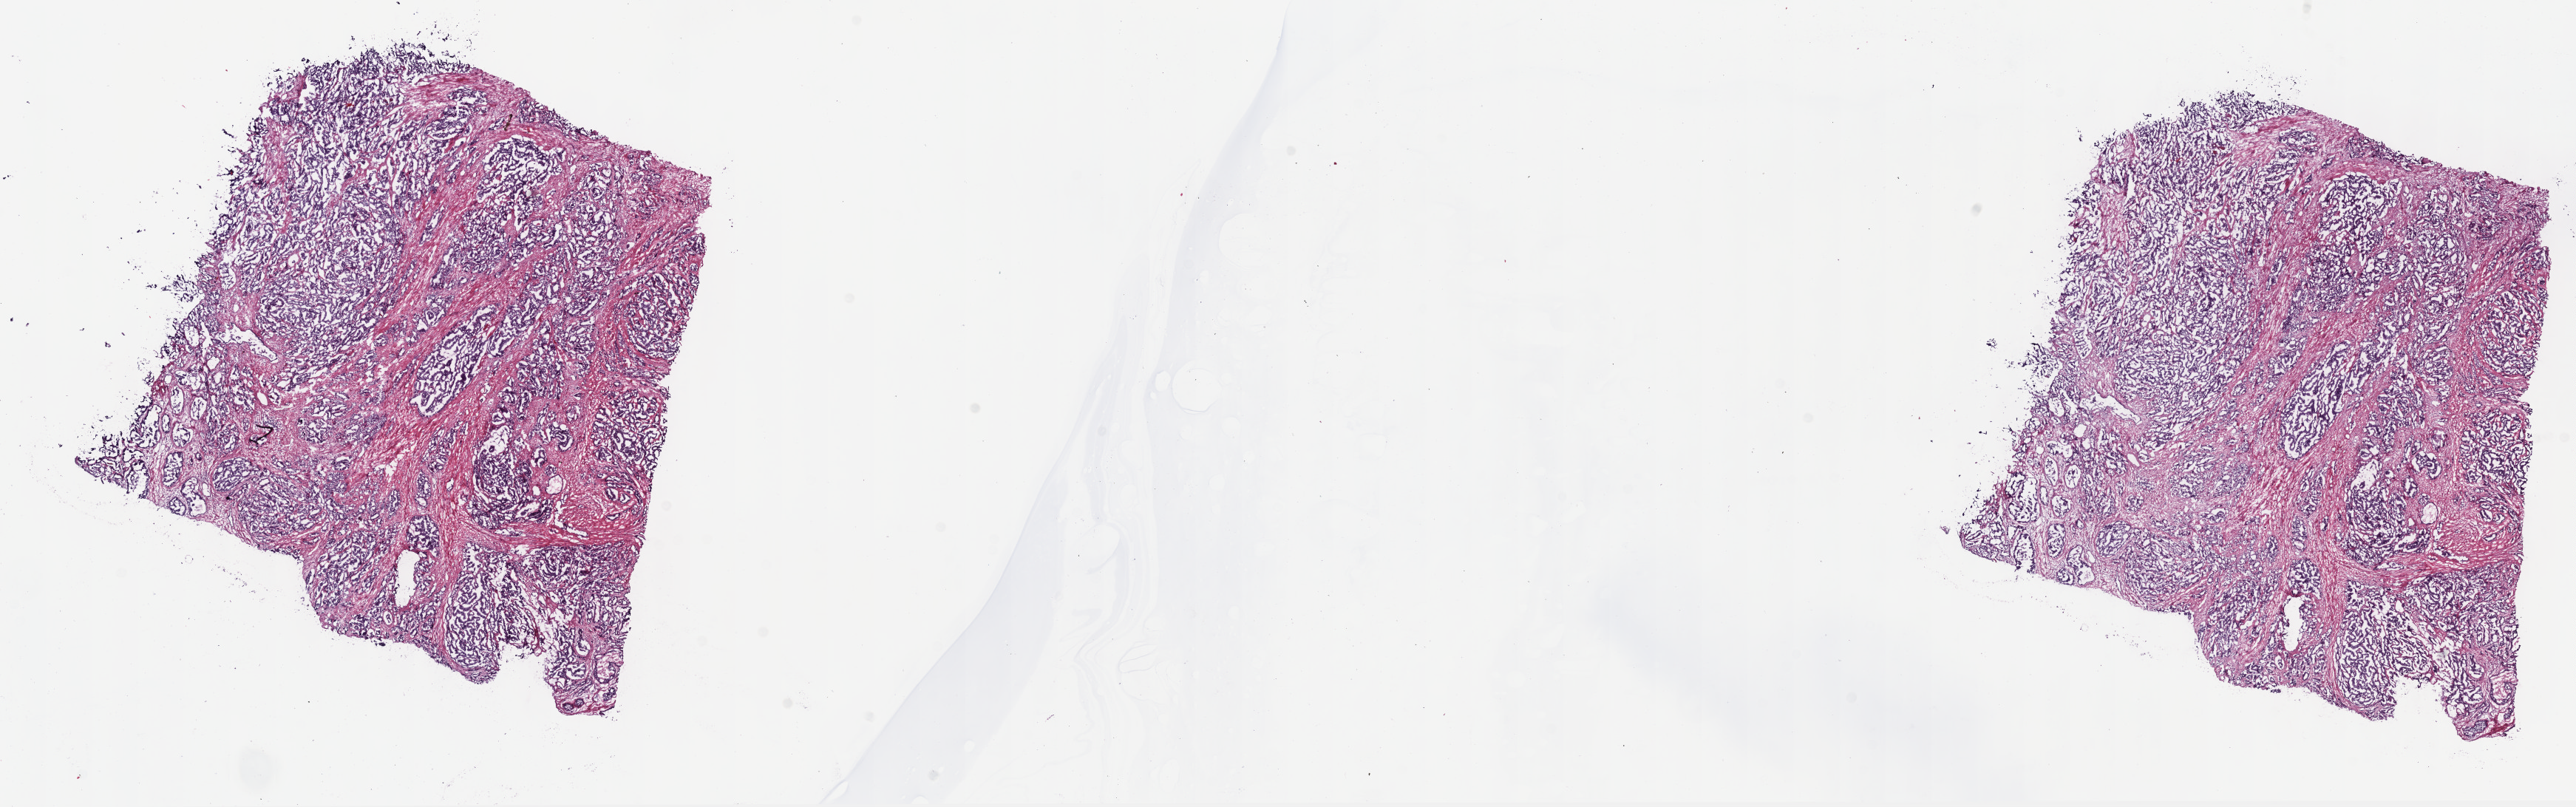
Whole-slide histology image, H&E-stained, a low-resolution overview of the entire scanned area, about 28.2 x 8.8 mm; frozen section from the top of the tissue portion; prostate, primary tumour sample. Patient: male, age at initial diagnosis 57 years. Gleason score: 7 (4+3). Composition of this section per pathologist review: tumour cells 80%, tumour nuclei 85%, normal cells 0%, stromal cells 20%, necrosis 0%. Inflammatory infiltration, as recorded: lymphocyte infiltration 0%, monocyte infiltration 0%, neutrophil infiltration 0%.
* pathologic diagnosis: Adenocarcinoma, NOS